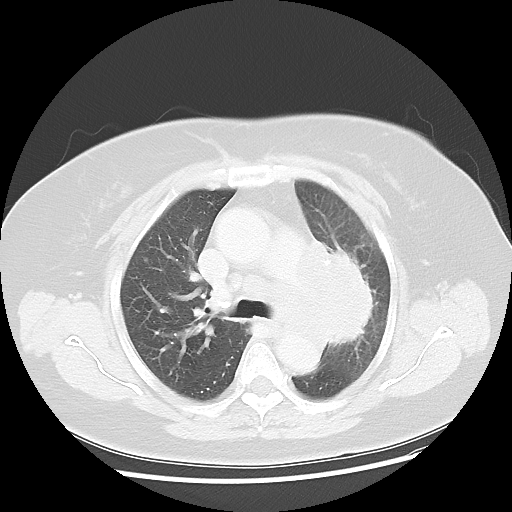
Chest CT, one axial slice; slice 31 of 49 in the series (ordered by position); lung window (W 1500 / L -600 HU); 5 mm slice thickness; 512 × 512 image matrix, field of view 374 × 374 mm. Female patient, age 58 years. From the clinical record (not read from this slice): clinical TNM (as recorded): T4 N3 M0.
Structures marked on this image (bounding box drawn by a radiologist):
- lung tumour (recorded histology: small cell carcinoma): bounding box [x1, y1, x2, y2] px = [281, 226, 375, 373]